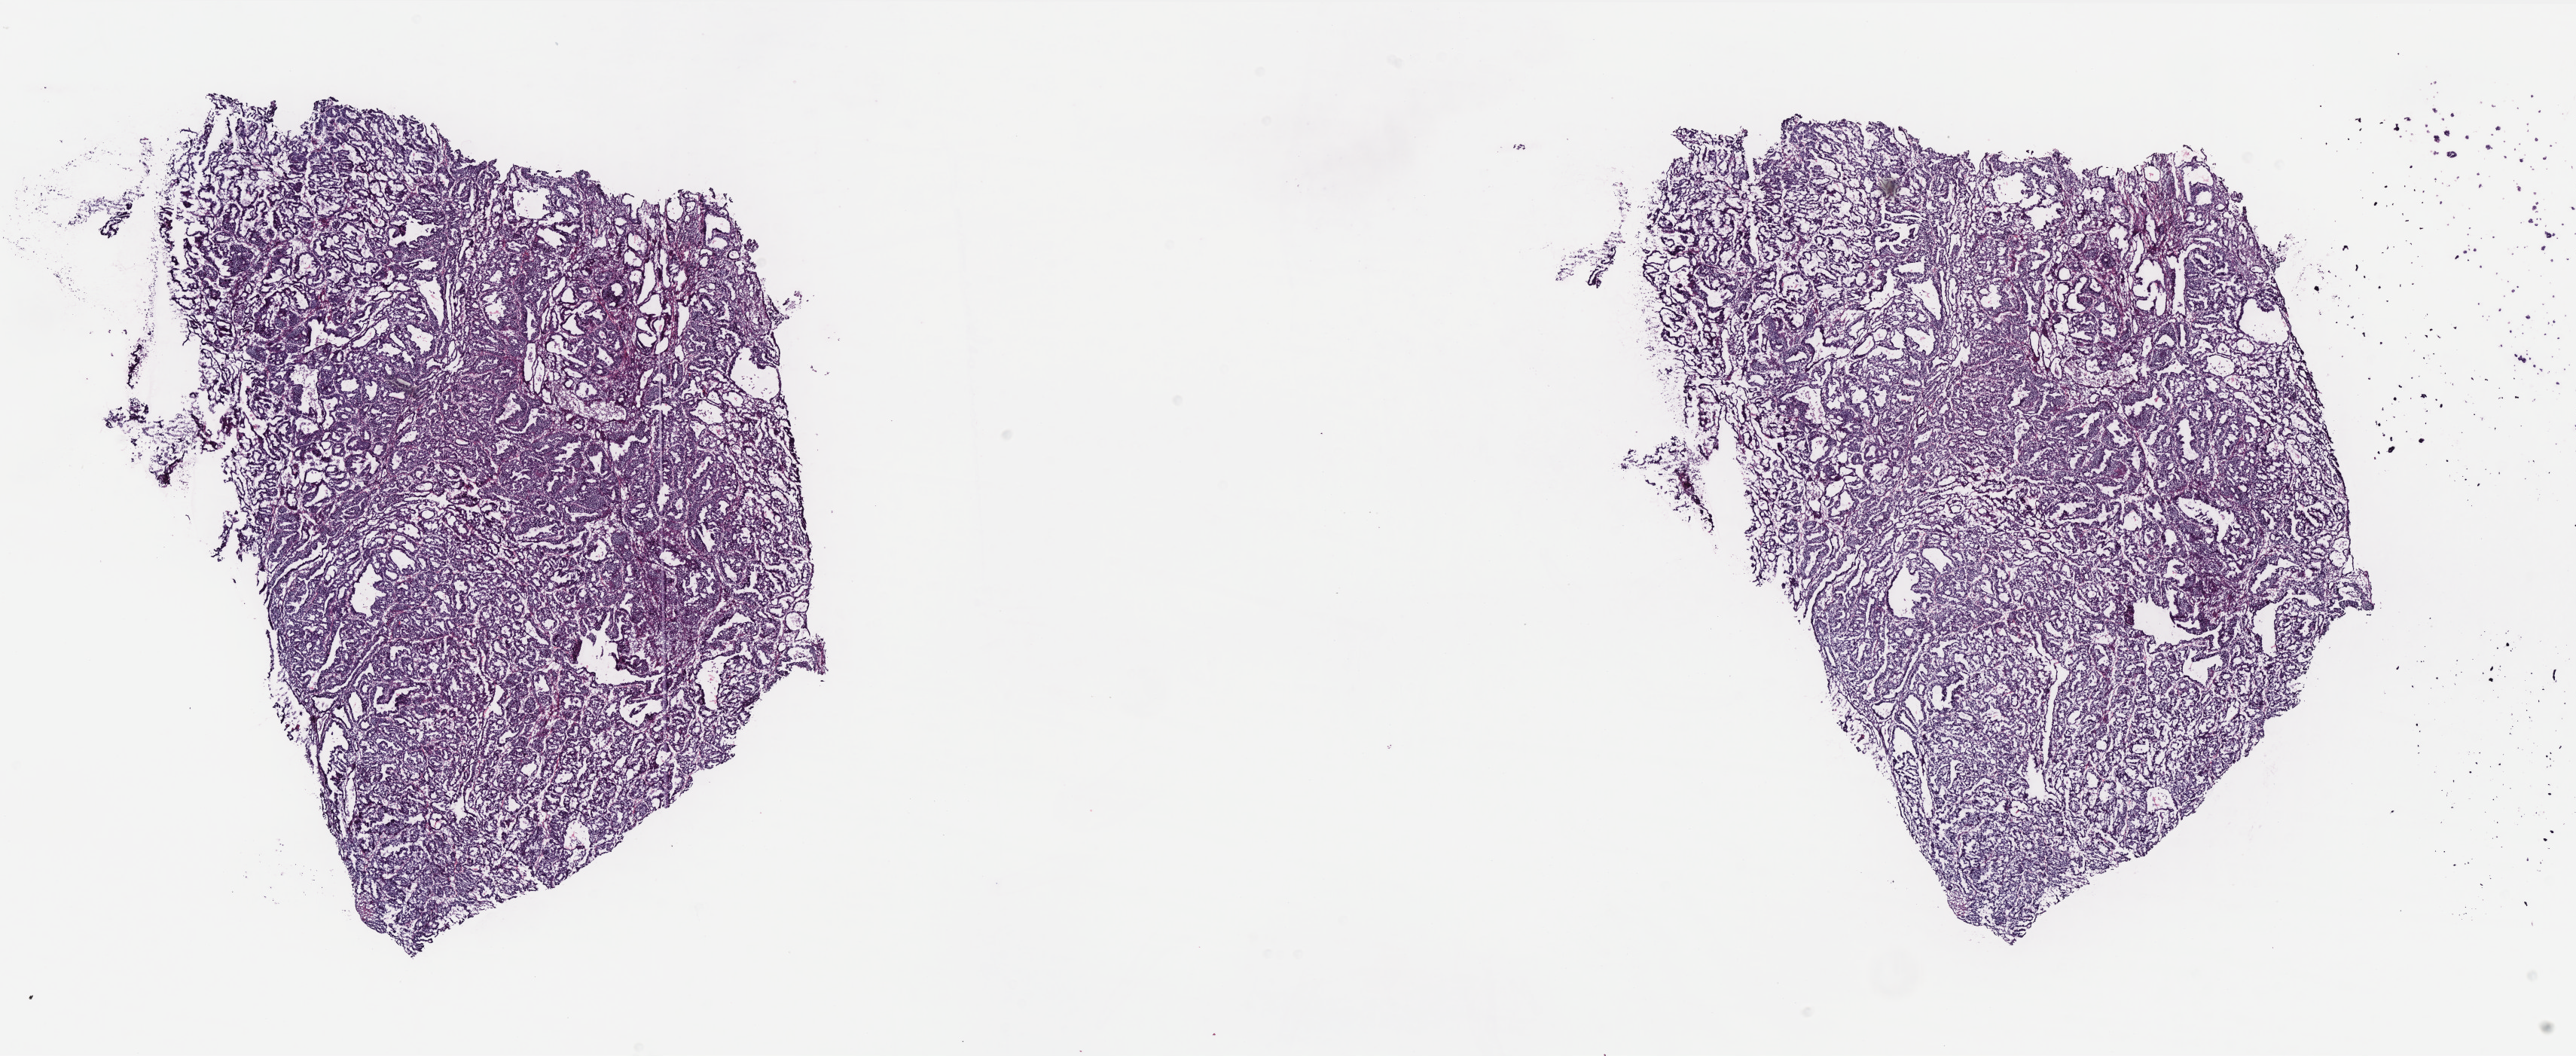
Digitized H&E-stained tissue section (whole slide) — whole scanned area (about 27.4 x 11.2 mm, from a 40x scan) shown as a low-resolution overview; frozen section from the bottom of the tissue portion; primary tumour sample from the uterus. Female patient; age at initial diagnosis 66 years. Histologic grade: G1 (well differentiated). Composition of this section per pathologist review: tumour cells 100%, tumour nuclei 95%, normal cells 0%, stromal cells 0%, necrosis 0%. Inflammatory infiltration, as recorded: lymphocyte infiltration 0%, monocyte infiltration 2%, neutrophil infiltration 2%.
* pathologic diagnosis: Endometrioid adenocarcinoma, NOS (endometrium)
* FIGO stage: IA